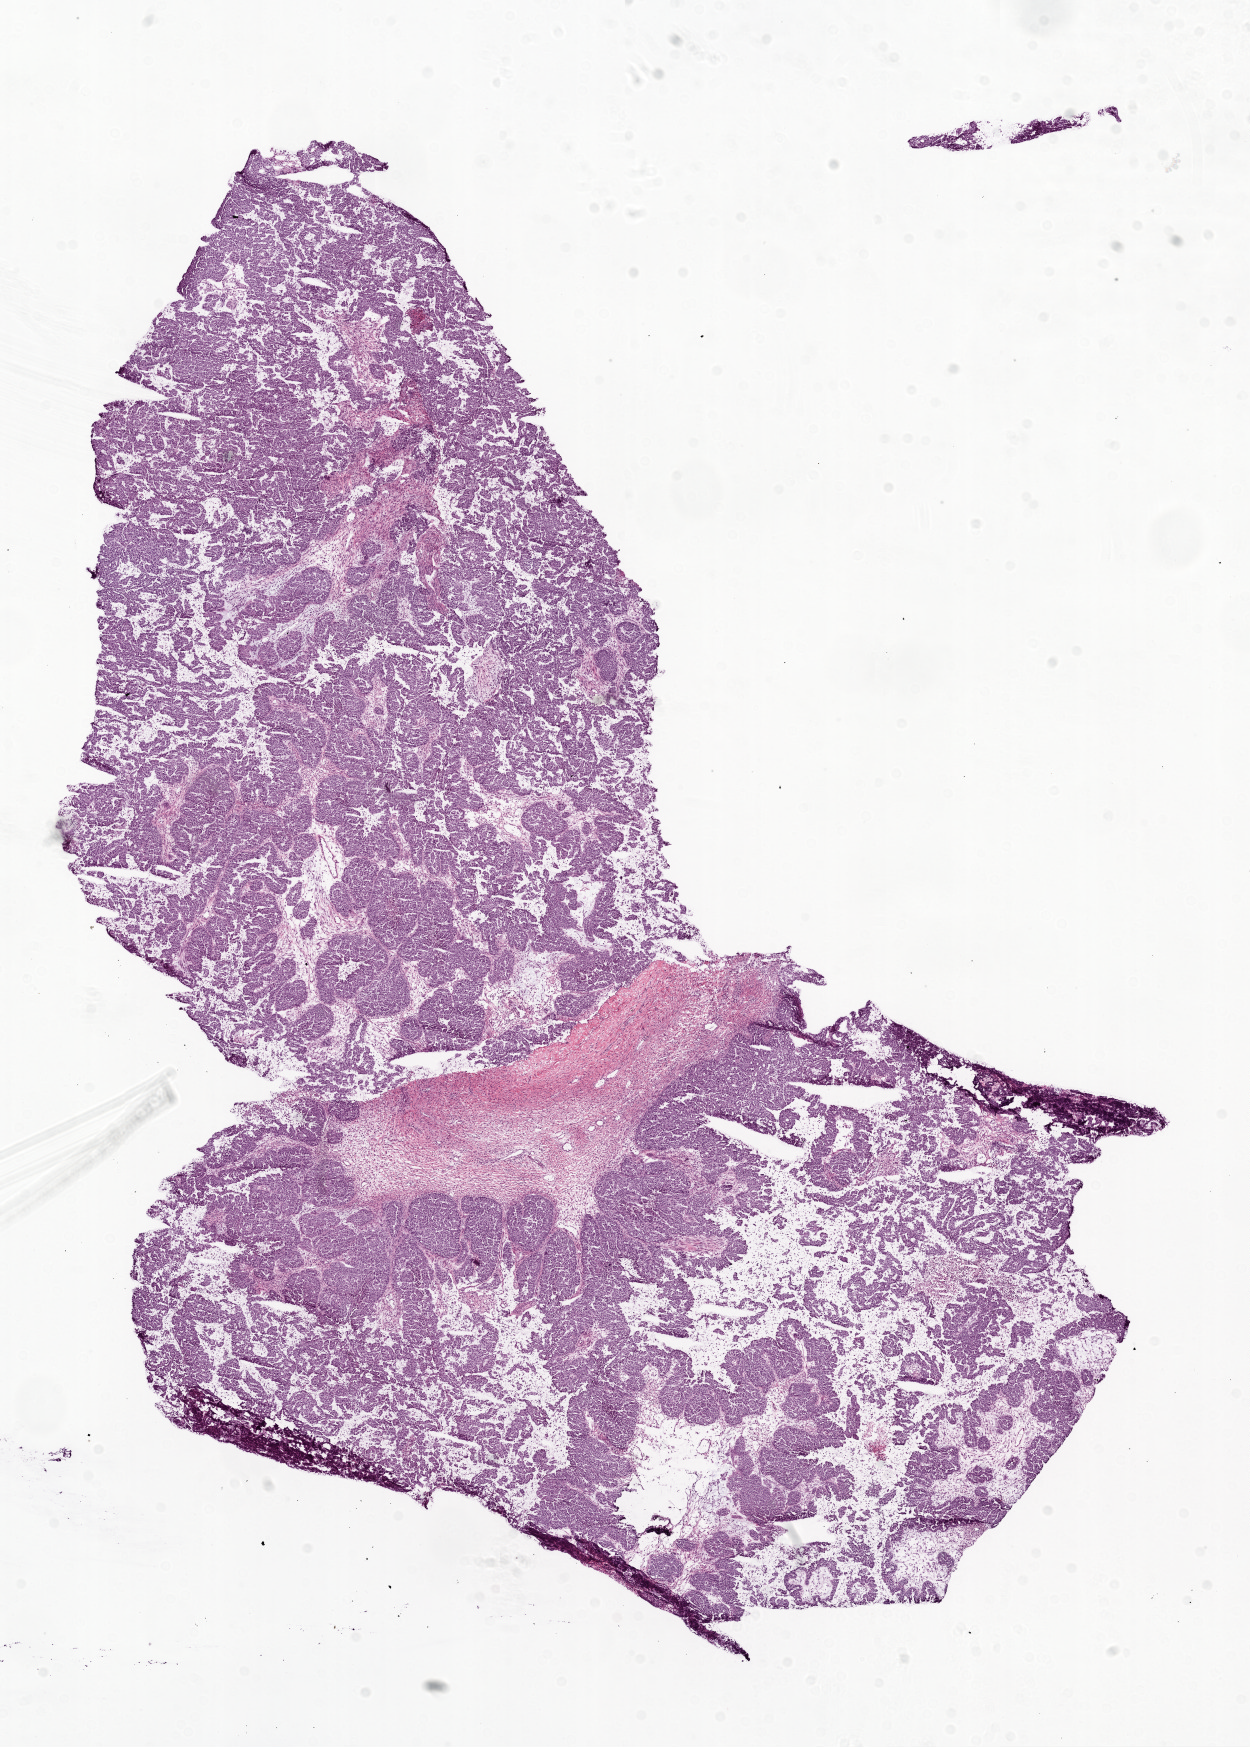
Whole-slide histology image, H&E-stained — shown as a low-resolution overview of the whole scanned area (about 10.0 x 14.0 mm, acquisition: 20x scan). Frozen section from the top of the tissue portion. Ovary, primary tumour sample. Female patient; age at initial diagnosis 40 years.
Diagnosis: Serous cystadenocarcinoma, NOS.